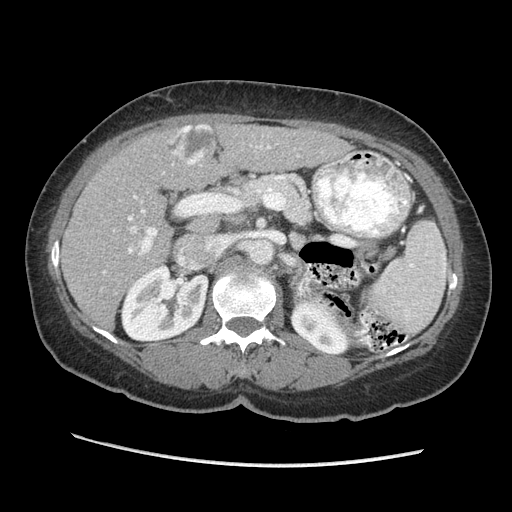
Contrast-enhanced abdominal CT (liver protocol), one axial slice; position 123 of 170 along the scan axis; reconstruction kernel STANDARD; 140 kVp; soft-tissue window (W 400 / L 40 HU); 2.5 mm slice thickness; 512 × 512 image matrix, field of view 360 × 360 mm. Case-level facts recorded for this patient, not image findings: diagnosis: hepatocellular carcinoma (patient treated with transarterial chemoembolisation; whether this scan precedes or follows treatment is not stated here); TNM stage (as recorded): Stage-II; Child-Pugh class: A; tumour differentiation: no biopsy; tumour nodularity: multinodular.
Annotated regions visible in this slice (semi-automatically segmented with operator editing):
- liver parenchyma outside the tumour (the mass and vessels are separate outlines, so this box may not span the whole liver): bounding box <62,122,351,326> (left, top, right, bottom; pixels)
- mass: <172,125,218,165>
- liver vessels: <103,145,349,274>